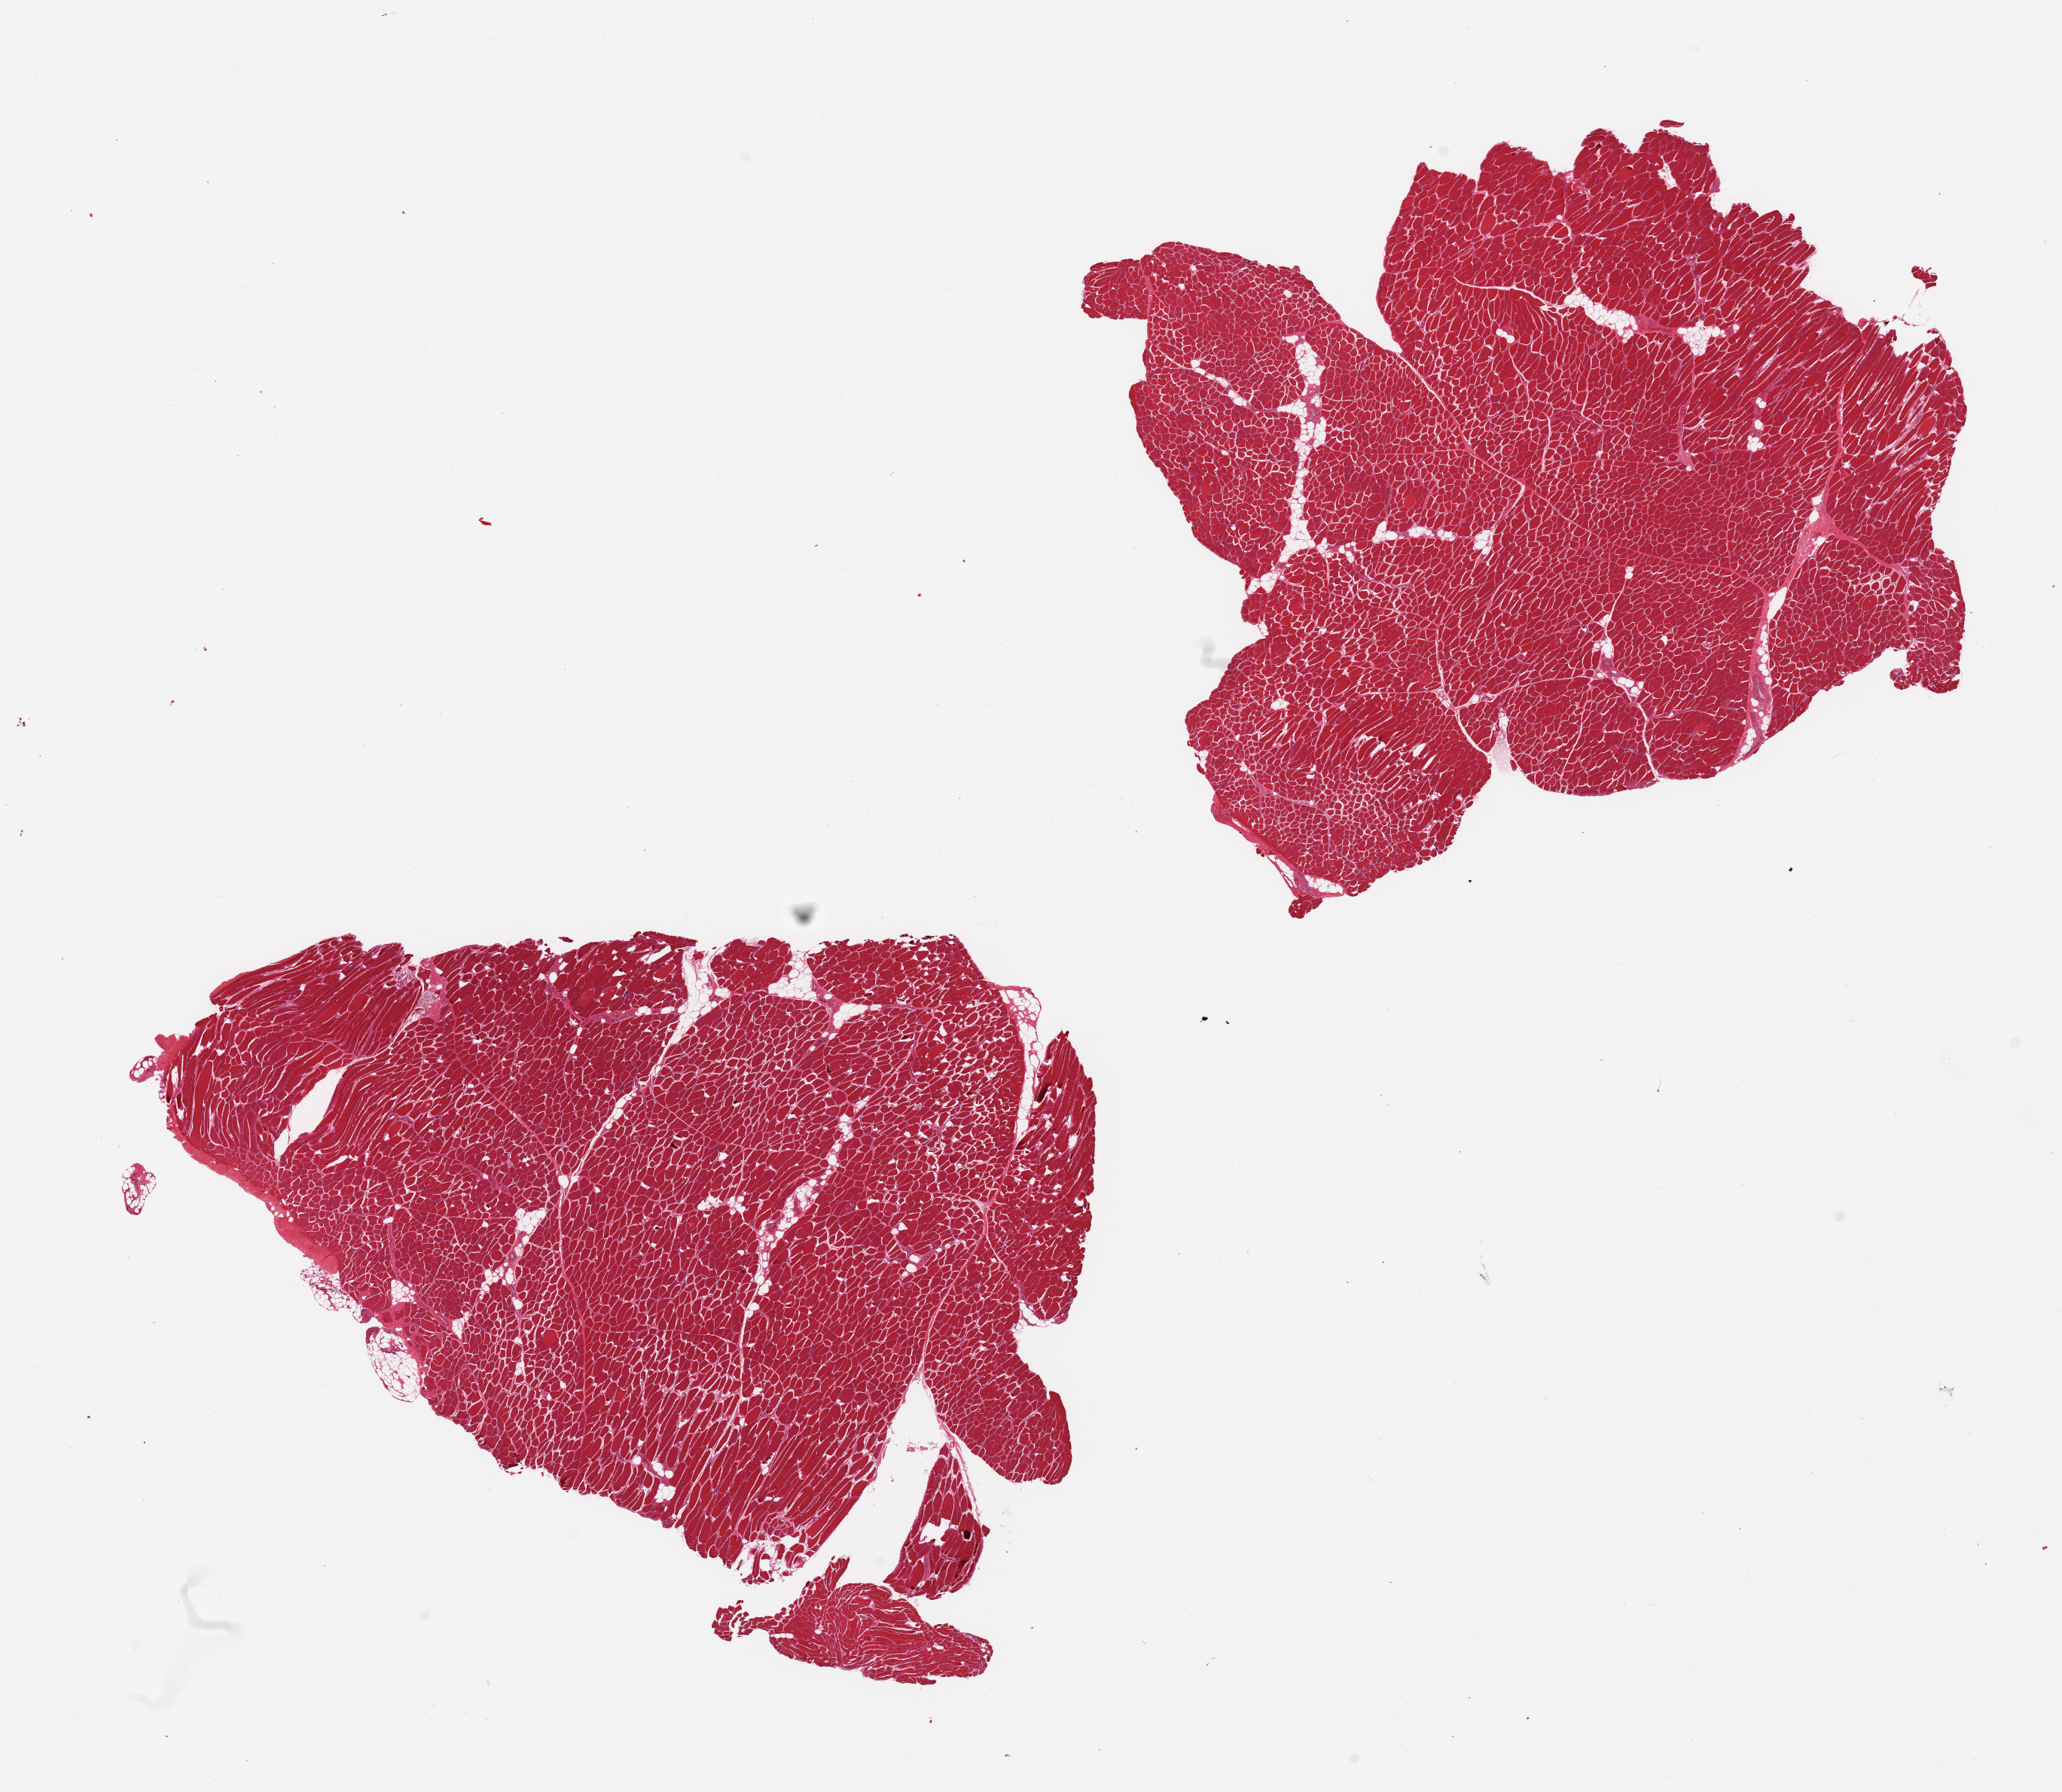
Digitized hematoxylin and eosin (H&E)-stained section, brightfield — a low-resolution overview of the entire scanned area, about 21.7 x 18.8 mm, PAXgene-fixed, paraffin-embedded tissue, section of skeletal muscle (target tissue), donor tissue sample.
Pathologist's review note for this sample: 2 pieces, ~5% adipose tissue.